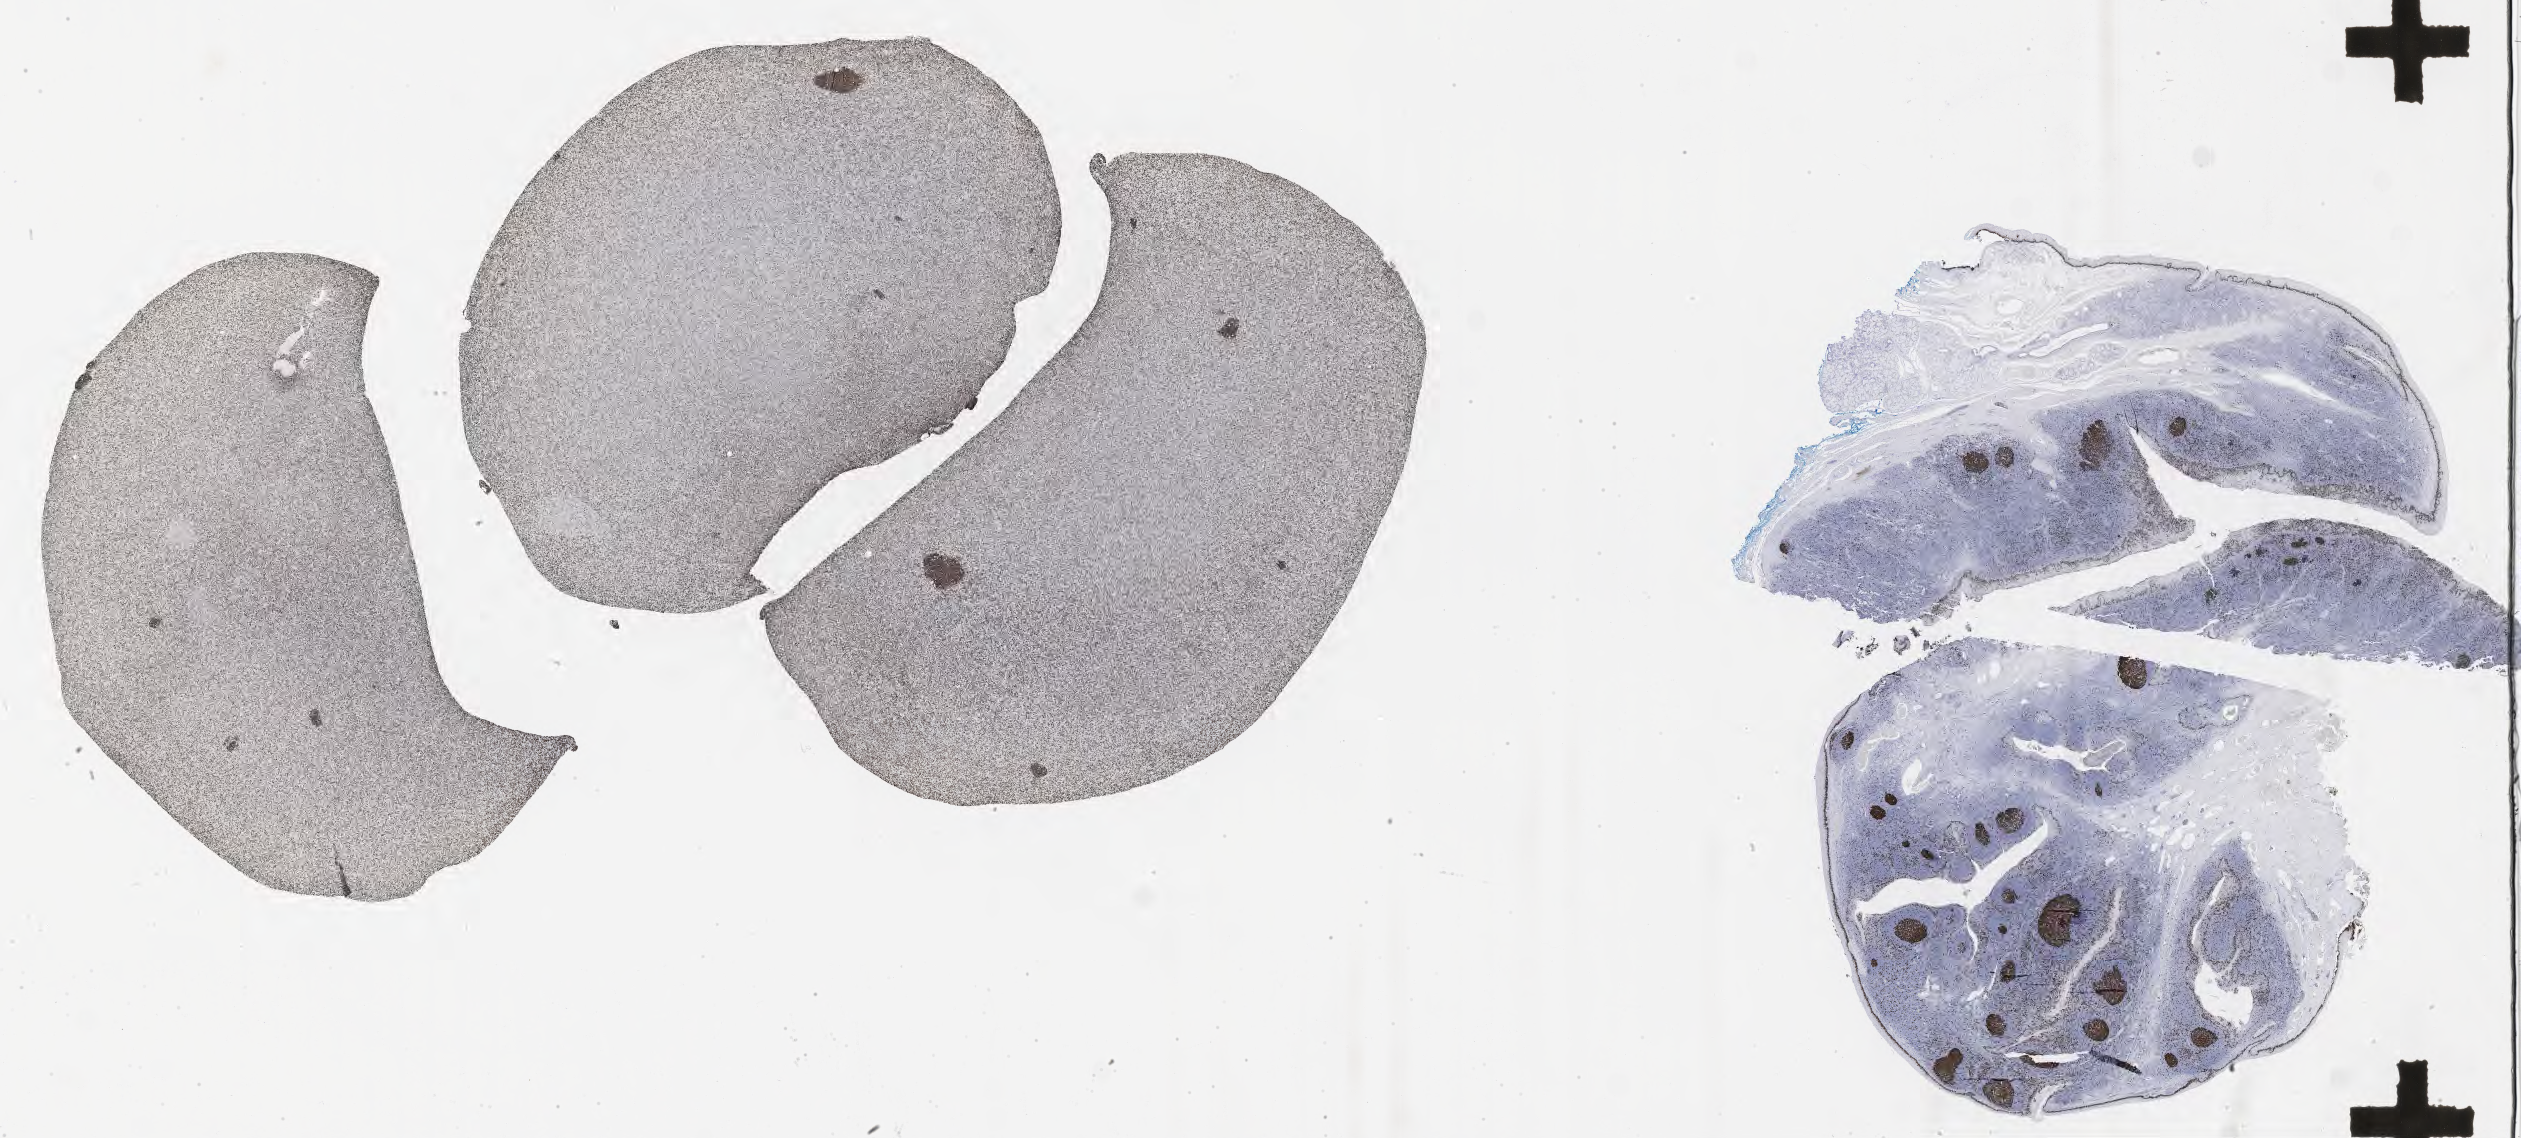
IHC for Ki-67, whole-slide image, shown as a low-resolution overview of the whole scanned area (about 40.8 x 18.4 mm). Tumor tissue. Male patient, aged 17.
Histologic diagnosis: Burkitt lymphoma, NOS.